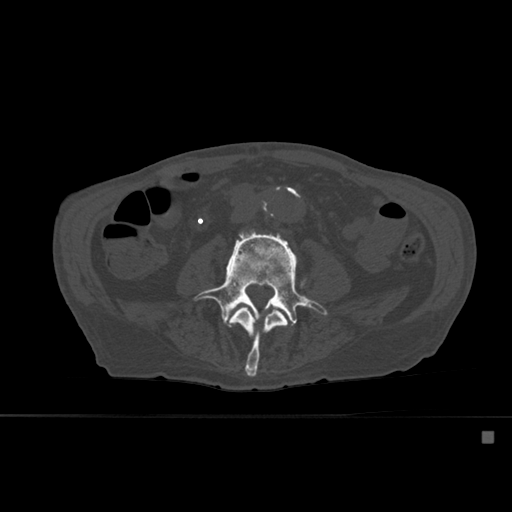
CT including the spine, one axial slice; position 200 of 527 along the scan axis; bone window (W 1800 / L 400 HU); 1.5 mm slice thickness; 512 × 512 image matrix. Patient: male, 78 years. Case-level facts recorded for this patient, not image findings: primary cancer: prostate.
Outlined on this slice (semi-automatically segmented with operator editing):
- L3 vertebra: bounding box [x1, y1, x2, y2] px = [228, 307, 288, 377]
- L4 vertebra: [194, 231, 328, 338]